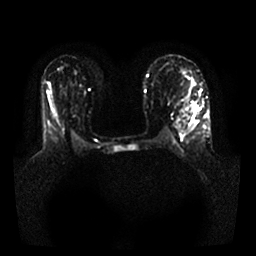
Breast MRI, one axial slice; slice 19 of 25 in the series (ordered by position); diffusion-weighted series; image 2 of 4 stored at this slice position (different b-values; order by instance number); 1.5 T; 4 mm slice thickness; 256 × 256 image matrix. Female patient.
Structures marked on this image (outlined manually by an expert reader):
- tumour on diffusion-weighted imaging: bounding box [x1, y1, x2, y2] px = [193, 104, 197, 110]